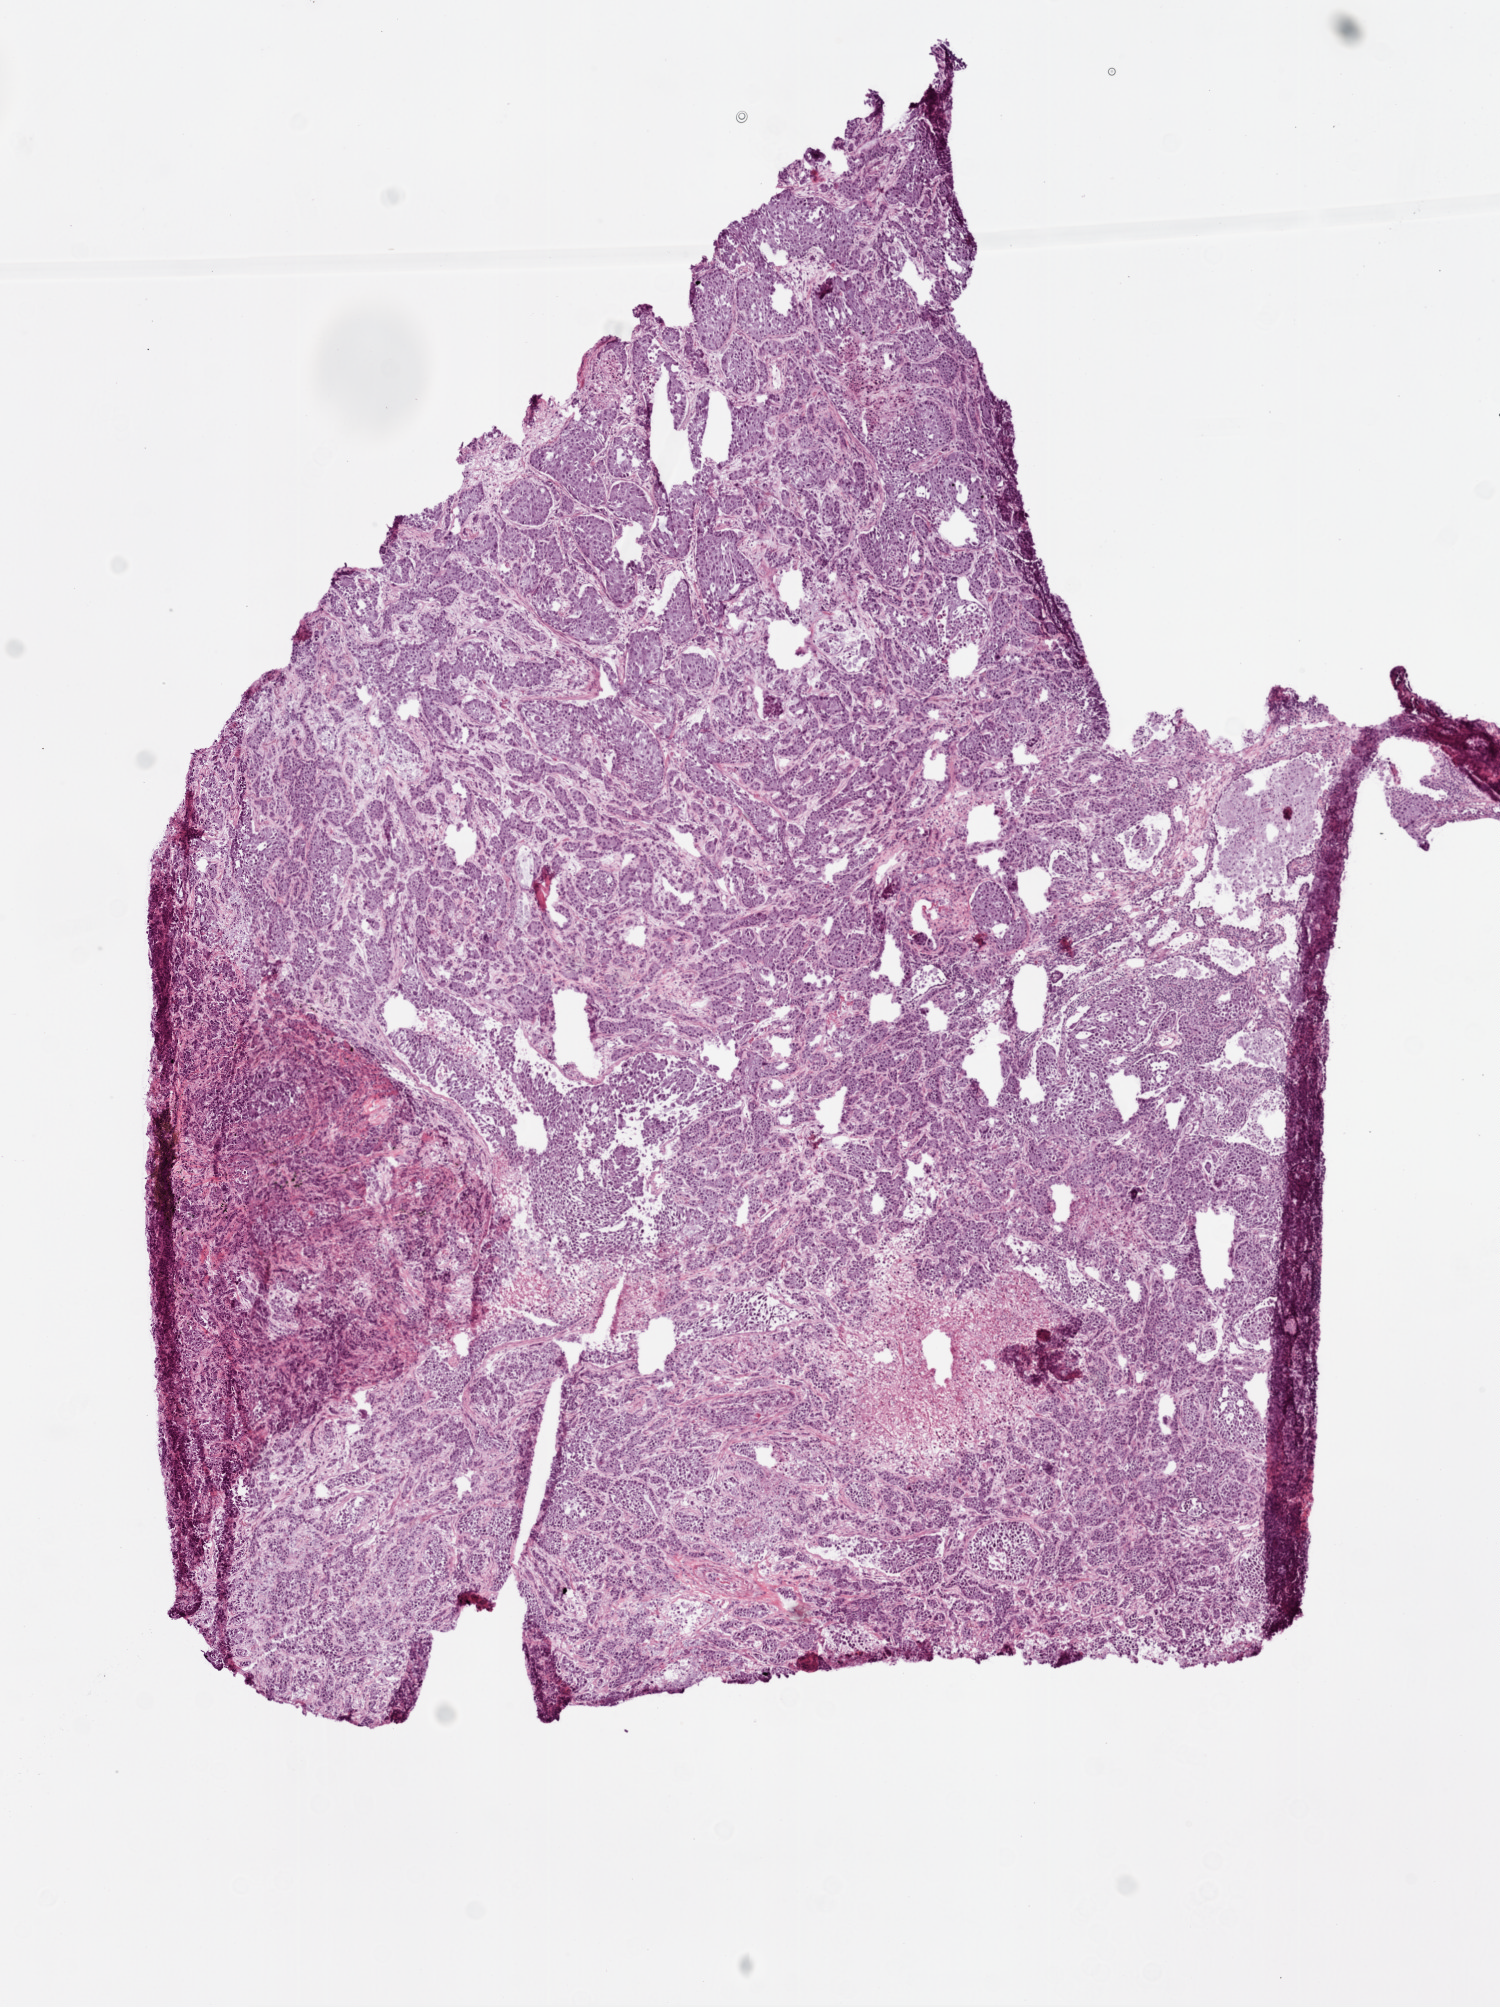
Hematoxylin and eosin (H&E) stained whole-slide image — low-resolution overview of the scanned area, about 6.0 x 8.1 mm (acquisition: 20x scan), frozen section from the top of the tissue portion, sample: primary tumour, lung. Patient: female, age at initial diagnosis 69 years. Composition of this section per pathologist review: tumour cells 95%, tumour nuclei 90%, normal cells 0%, stromal cells 0%, necrosis 5%.
• histologic diagnosis: Adenocarcinoma, NOS (upper lobe, lung)
• AJCC pathologic stage: IV